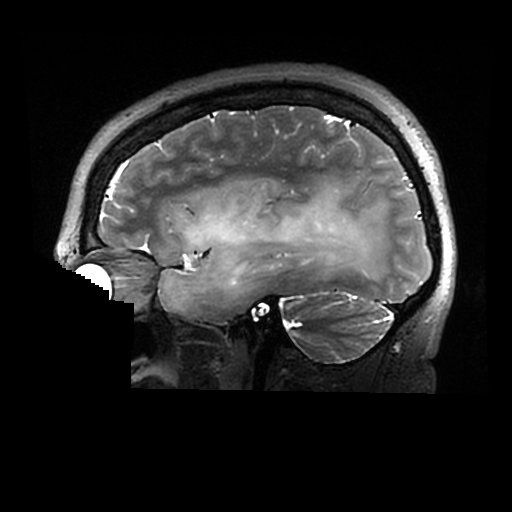
Brain MRI from a brain-tumour surgery series, one sagittal slice. Slice 209 of 320 in the series (ordered by position). 0.6 mm slice thickness. 512 × 512 image matrix, field of view 240 × 240 mm. From the clinical record (not read from this slice): histopathology: Astrocytoma; WHO grade: 2; IDH mutation: yes.
Structures marked on this image (expert manual segmentation):
- tumour: bounding box <158,179,386,312> (left, top, right, bottom; pixels)